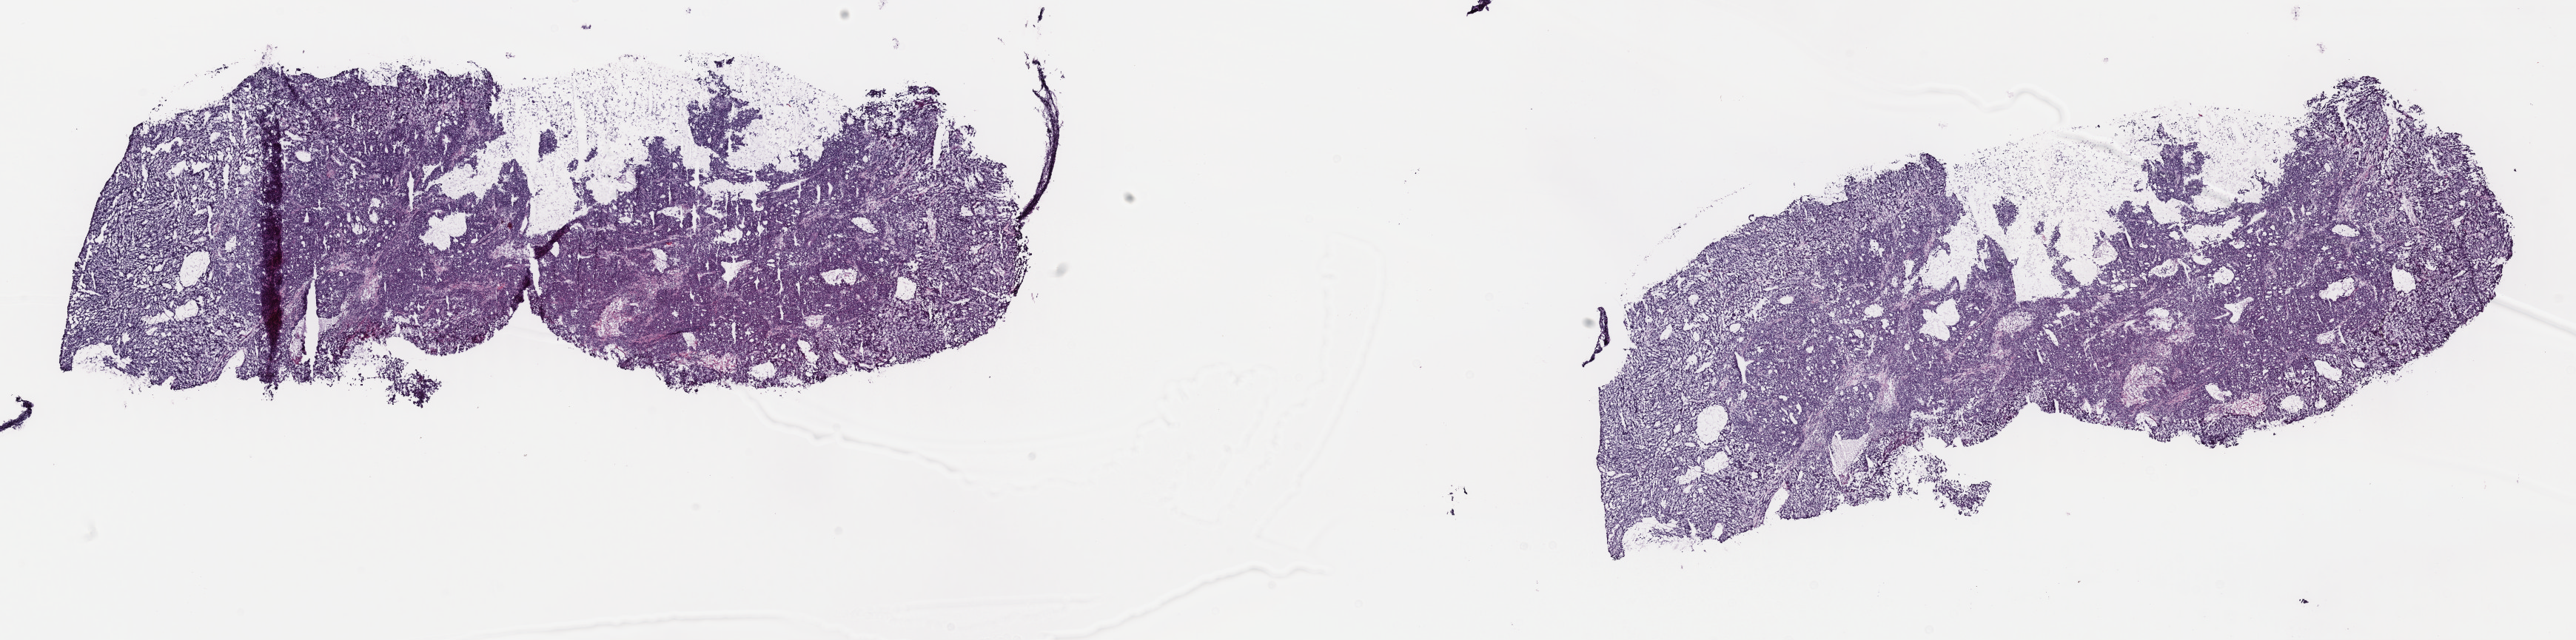
Digitized H&E tissue section (whole slide) — low-resolution overview of the scanned area, about 27.5 x 6.8 mm. Frozen section from the top of the tissue portion. Sample: primary tumour, liver. Female patient; age at initial diagnosis 75 years. Histologic grade: G3 (poorly differentiated). Pathologist review of this section (percent, as recorded): tumour cells 96%, tumour nuclei 94%, normal cells 0%, stromal cells 3%, necrosis 1%. Infiltration values recorded for this section: lymphocyte infiltration 5%, monocyte infiltration 1%, neutrophil infiltration 1%.
* AJCC pathologic stage: II (7th edition)
* diagnosis: Hepatocellular carcinoma, NOS